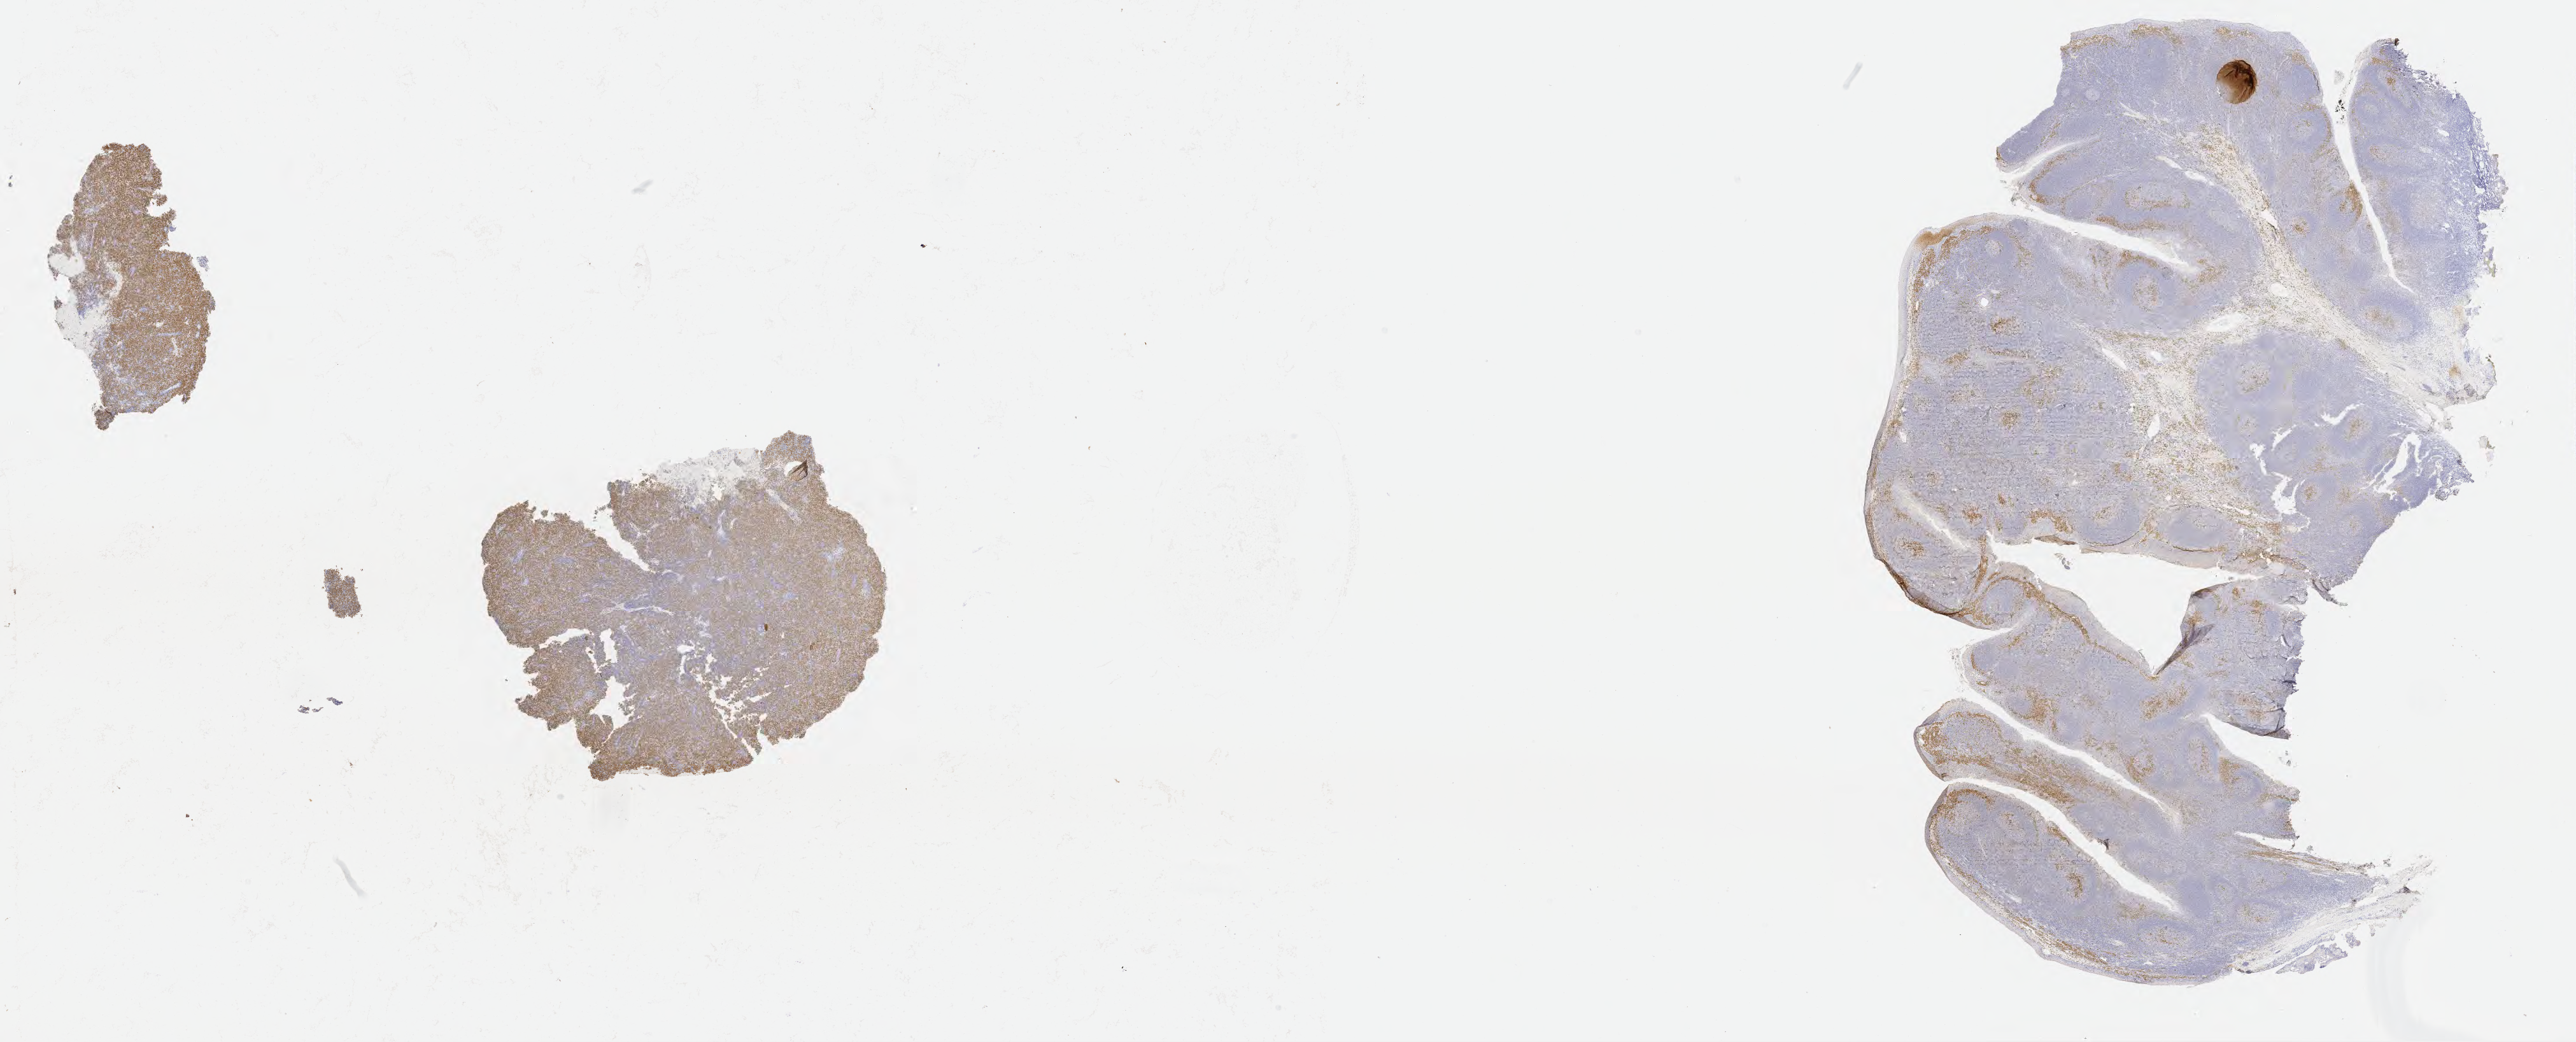
Whole-slide image, immunohistochemical stain for IRF4/MUM1 — whole scanned area (about 32.7 x 13.2 mm) shown as a low-resolution overview, specimen: tumor tissue, site: lymph node. Patient female; age 51 years.
Diagnosis: Diffuse large B-cell lymphoma, NOS.